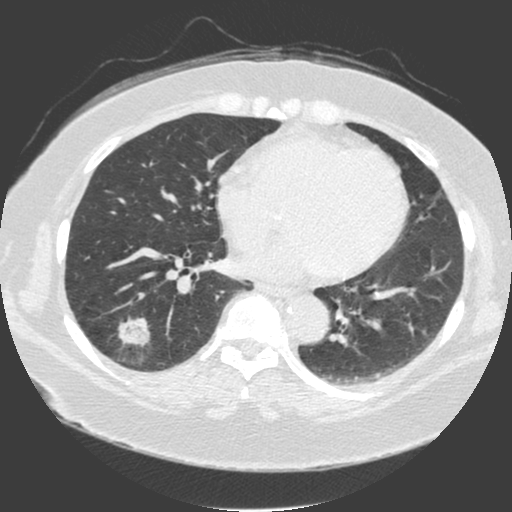
Low-dose screening chest CT, one axial slice. Slice 77 of 175 in the series (ordered by position). 120 kVp. Lung window (W 1500 / L -600 HU). 2 mm slice thickness. 512 × 512 image matrix, field of view 370 × 370 mm.
Outlined on this slice (manually delineated by an expert):
- lesion 1 (tumor, lower lobe of right lung): bounding box <119,318,150,346> (left, top, right, bottom; pixels)